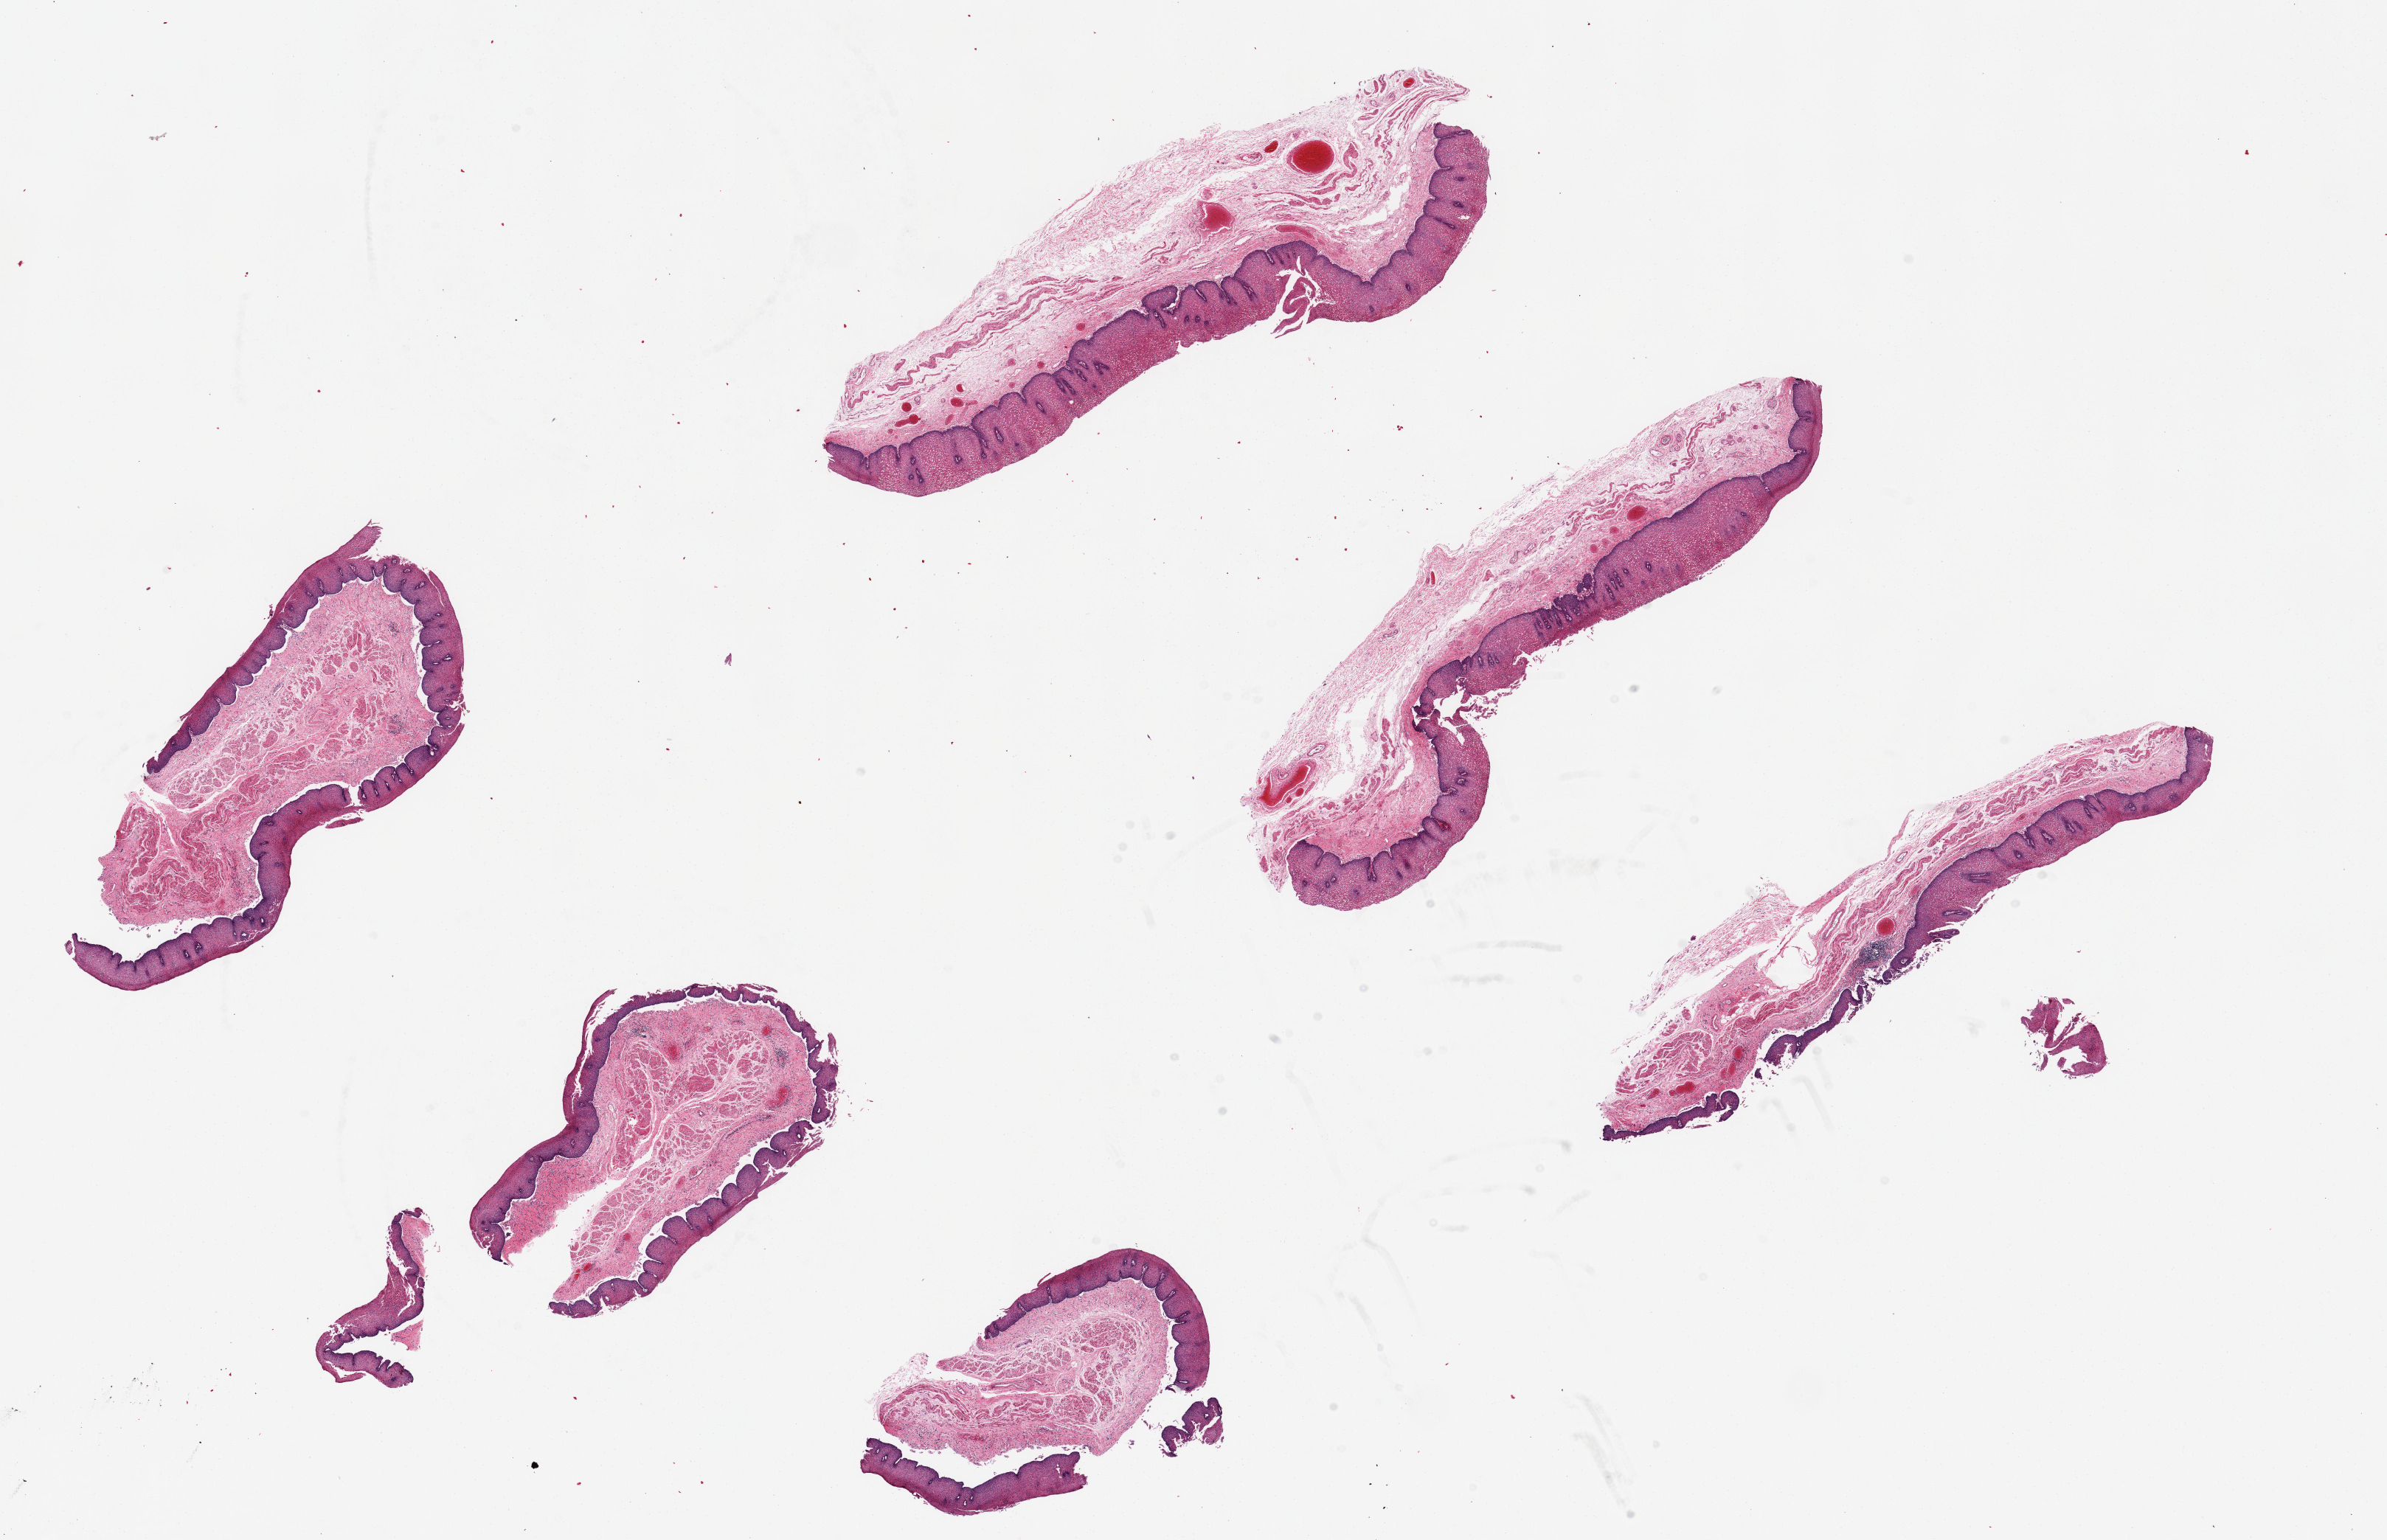
H&E whole-slide image, shown as a low-resolution overview of the whole scanned area (about 25.6 x 16.5 mm), PAXgene-fixed, paraffin-embedded tissue, section of esophageal mucous membrane (target tissue), tissue donor sample. Donor: male.
Reviewer comment on this tissue sample: 6 pieces, , ~5???7x1.5mm. Squamous mucosa is ~30% of thicknes14.